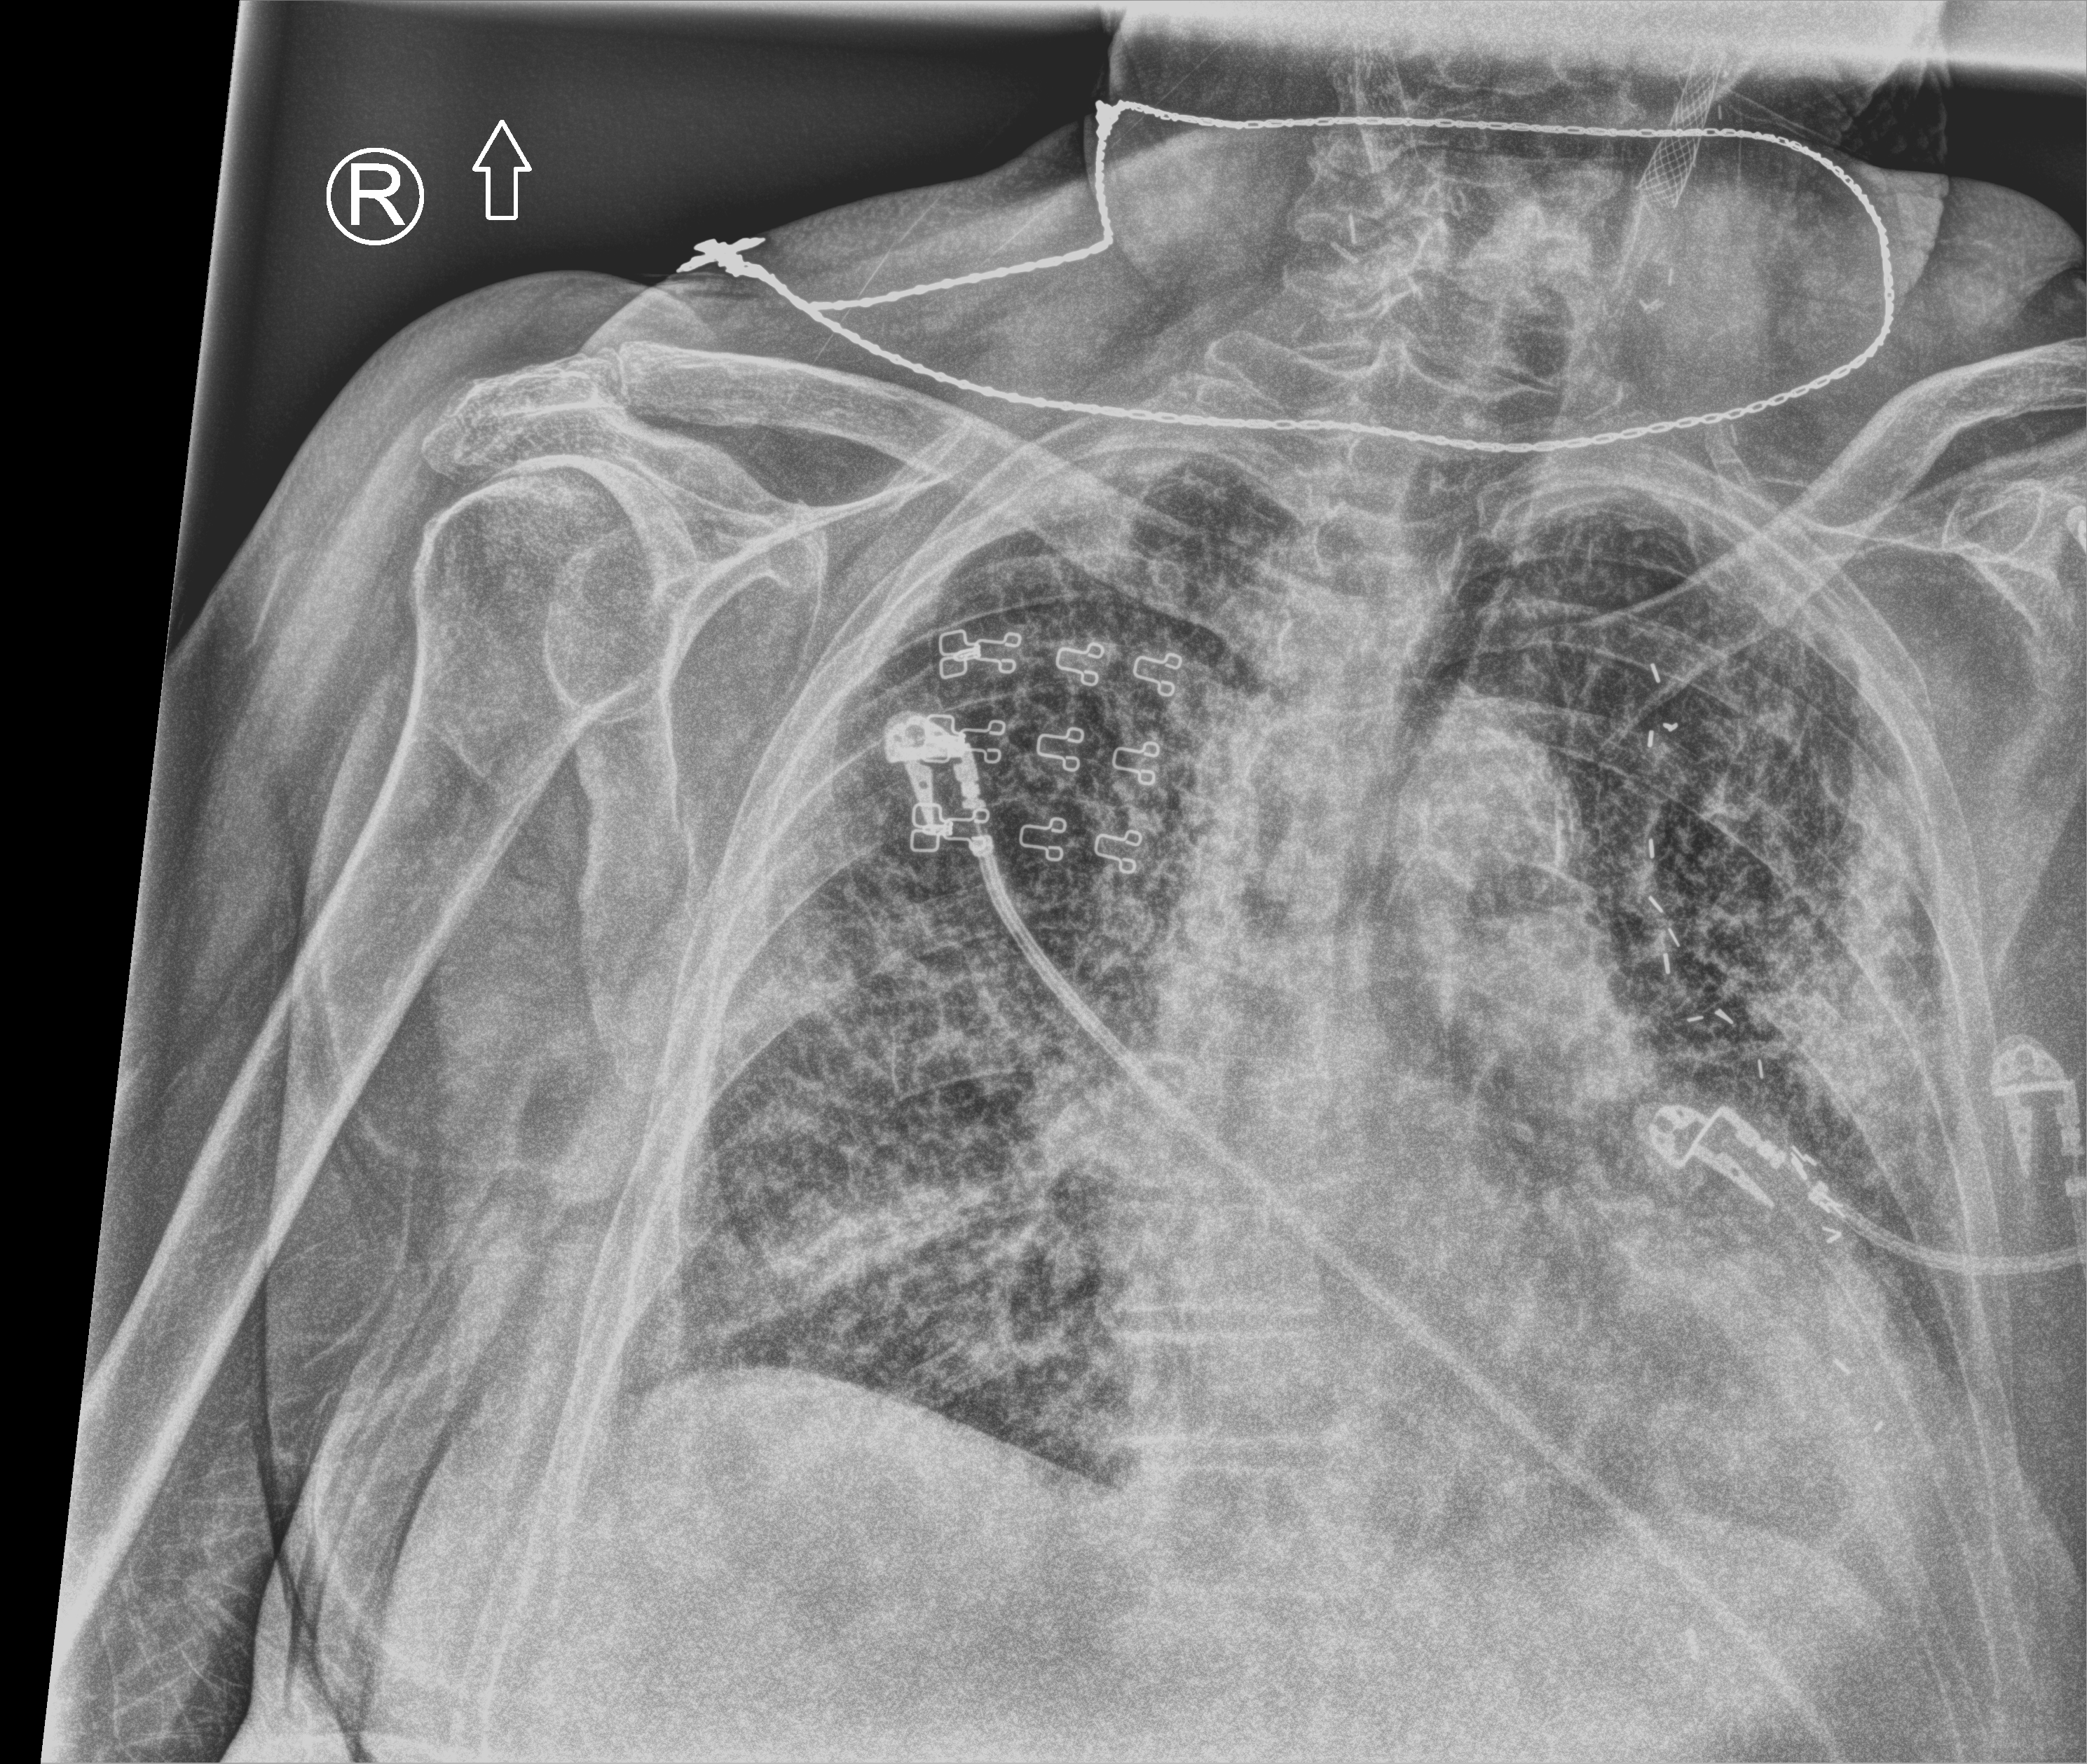
Chest X-ray (portable). Female patient hospitalised with COVID-19, age 75–90 years.
From the hospital-stay record, not from the radiograph (when in the stay this image was taken is not recorded): smoking status (admission record): former; chronic kidney disease (admission record): no; hypertension (admission record): no.